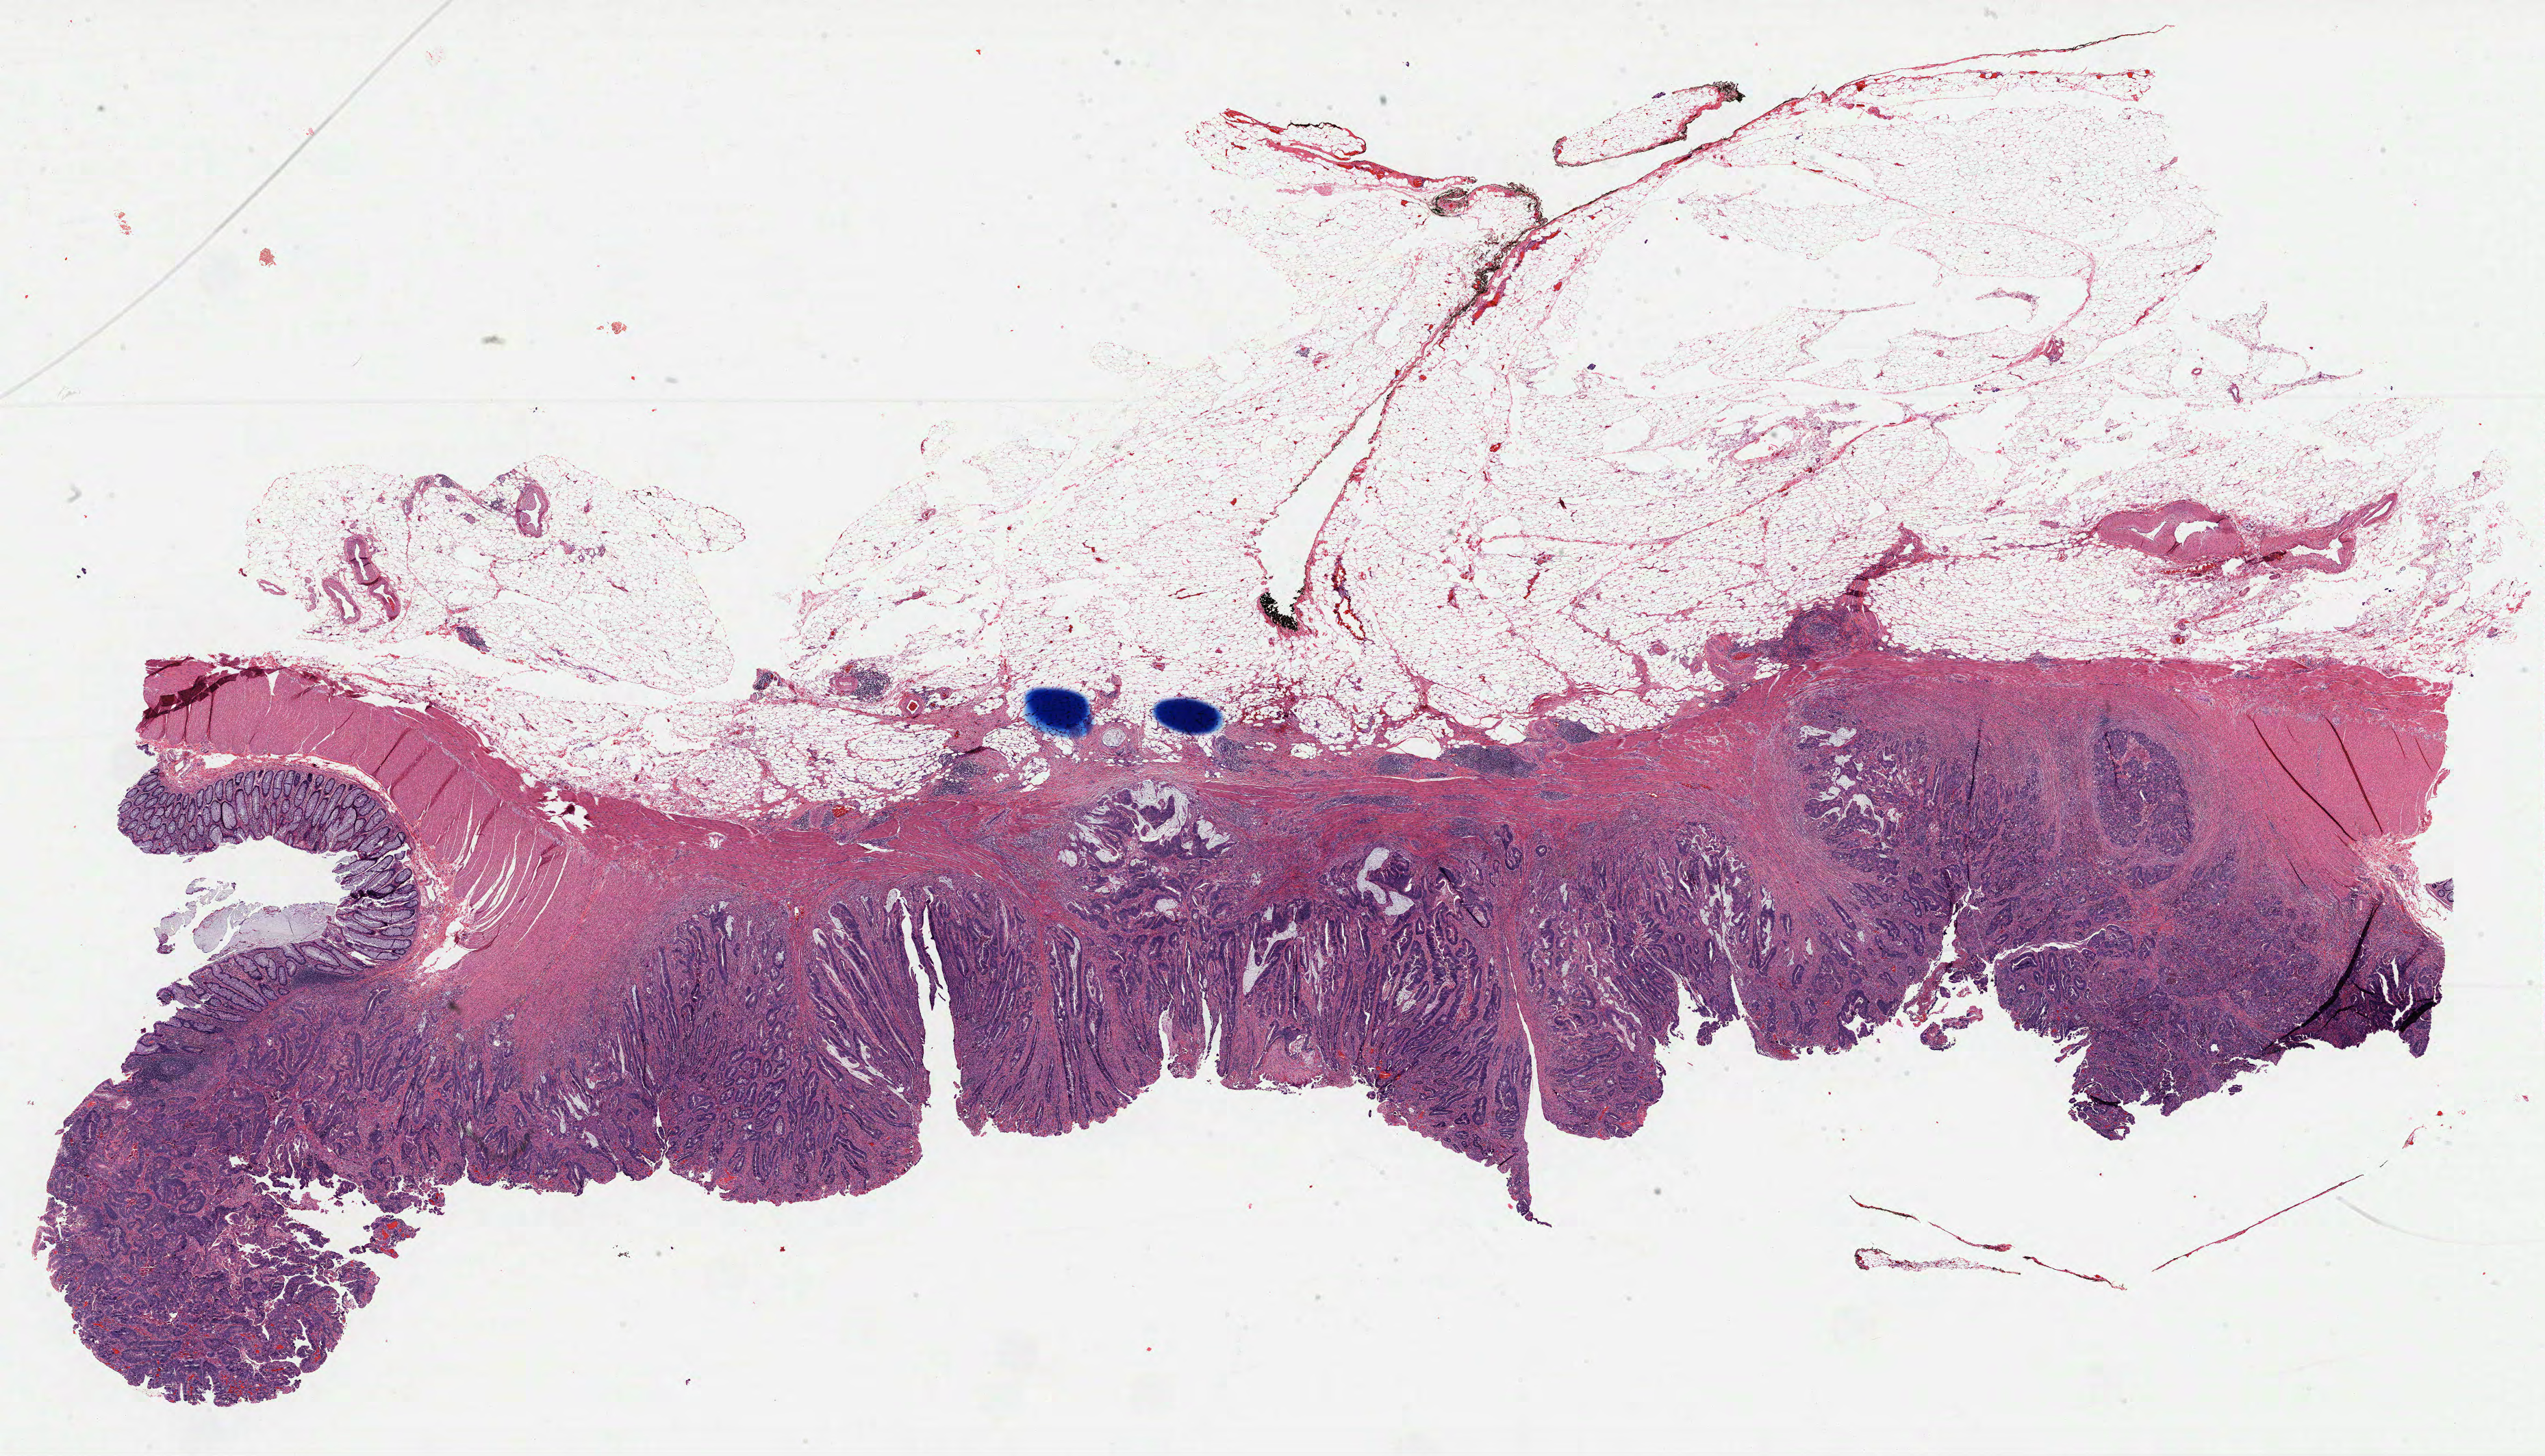
Whole-slide histology image, Hematoxylin and eosin (H&E) stained — low-resolution overview of the scanned area, about 30.0 x 17.2 mm (from a 40x scan). FFPE section. Primary tumour sample from the colon. Female patient; age at initial diagnosis 45 years.
Lymph nodes positive (case pathology): 3 of 20 examined. Pathologic diagnosis: Adenocarcinoma, NOS (sigmoid colon). AJCC pathologic stage: III (5th edition).